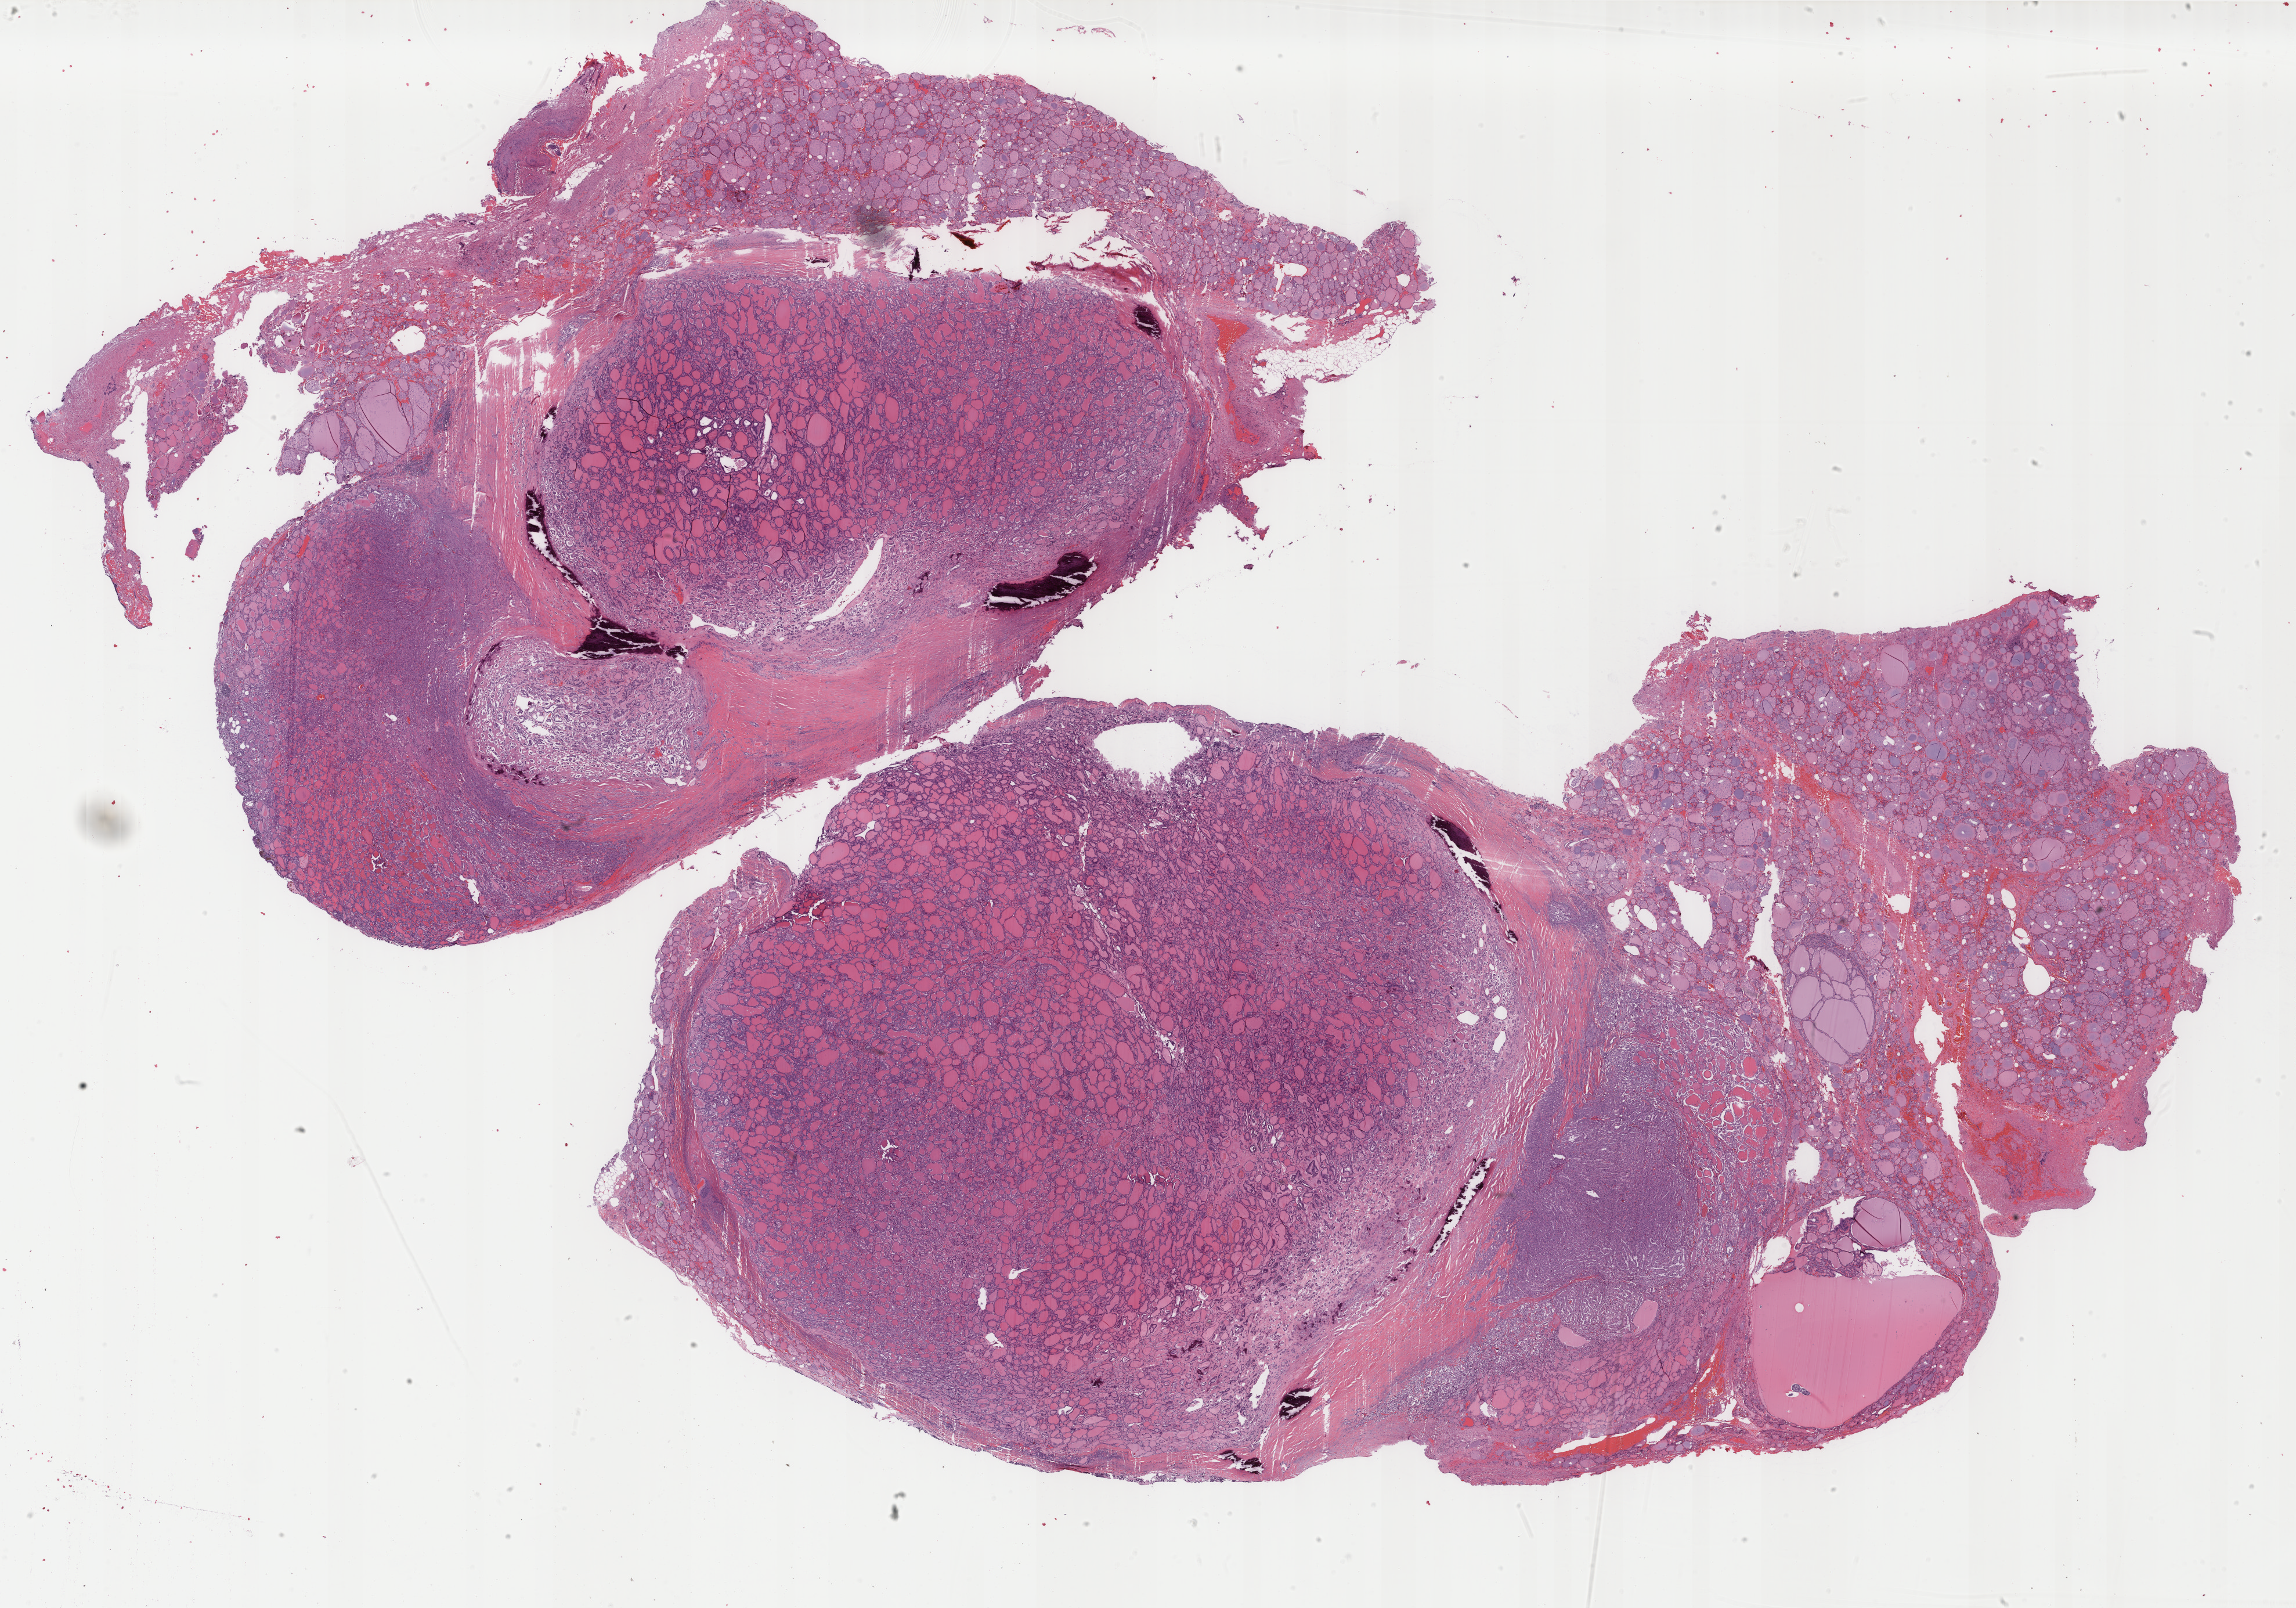
Whole-slide histology image, Hematoxylin and eosin (H&E) stained, shown as a low-resolution overview of the whole scanned area (about 31.4 x 22.0 mm, slide scanned at 40x), formalin-fixed paraffin-embedded (FFPE) diagnostic section, thyroid, primary tumour sample. Female patient; age at initial diagnosis 72 years.
Pathologic diagnosis: Papillary carcinoma, follicular variant.